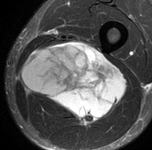
MRI of an extremity soft-tissue mass, one axial slice. Slice 49 of 90 in the series (ordered by position). STIR. MR volume resampled by the dataset authors to the PET/CT grid (not the native acquisition matrix). 3.27 mm slice thickness. 152 × 150 image matrix. Male patient. Case-level facts recorded for this patient, not image findings: histological type: undifferentiated pleomorphic liposarcoma; grade: high; site of the primary tumour: left thigh.
Outlined on this slice (expert contour drawn on MRI and transferred to this co-registered scan by the dataset authors):
- gross tumour volume including surrounding oedema: bounding box <22,43,128,127> (left, top, right, bottom; pixels)
- gross tumour volume (mass): <23,43,128,127>